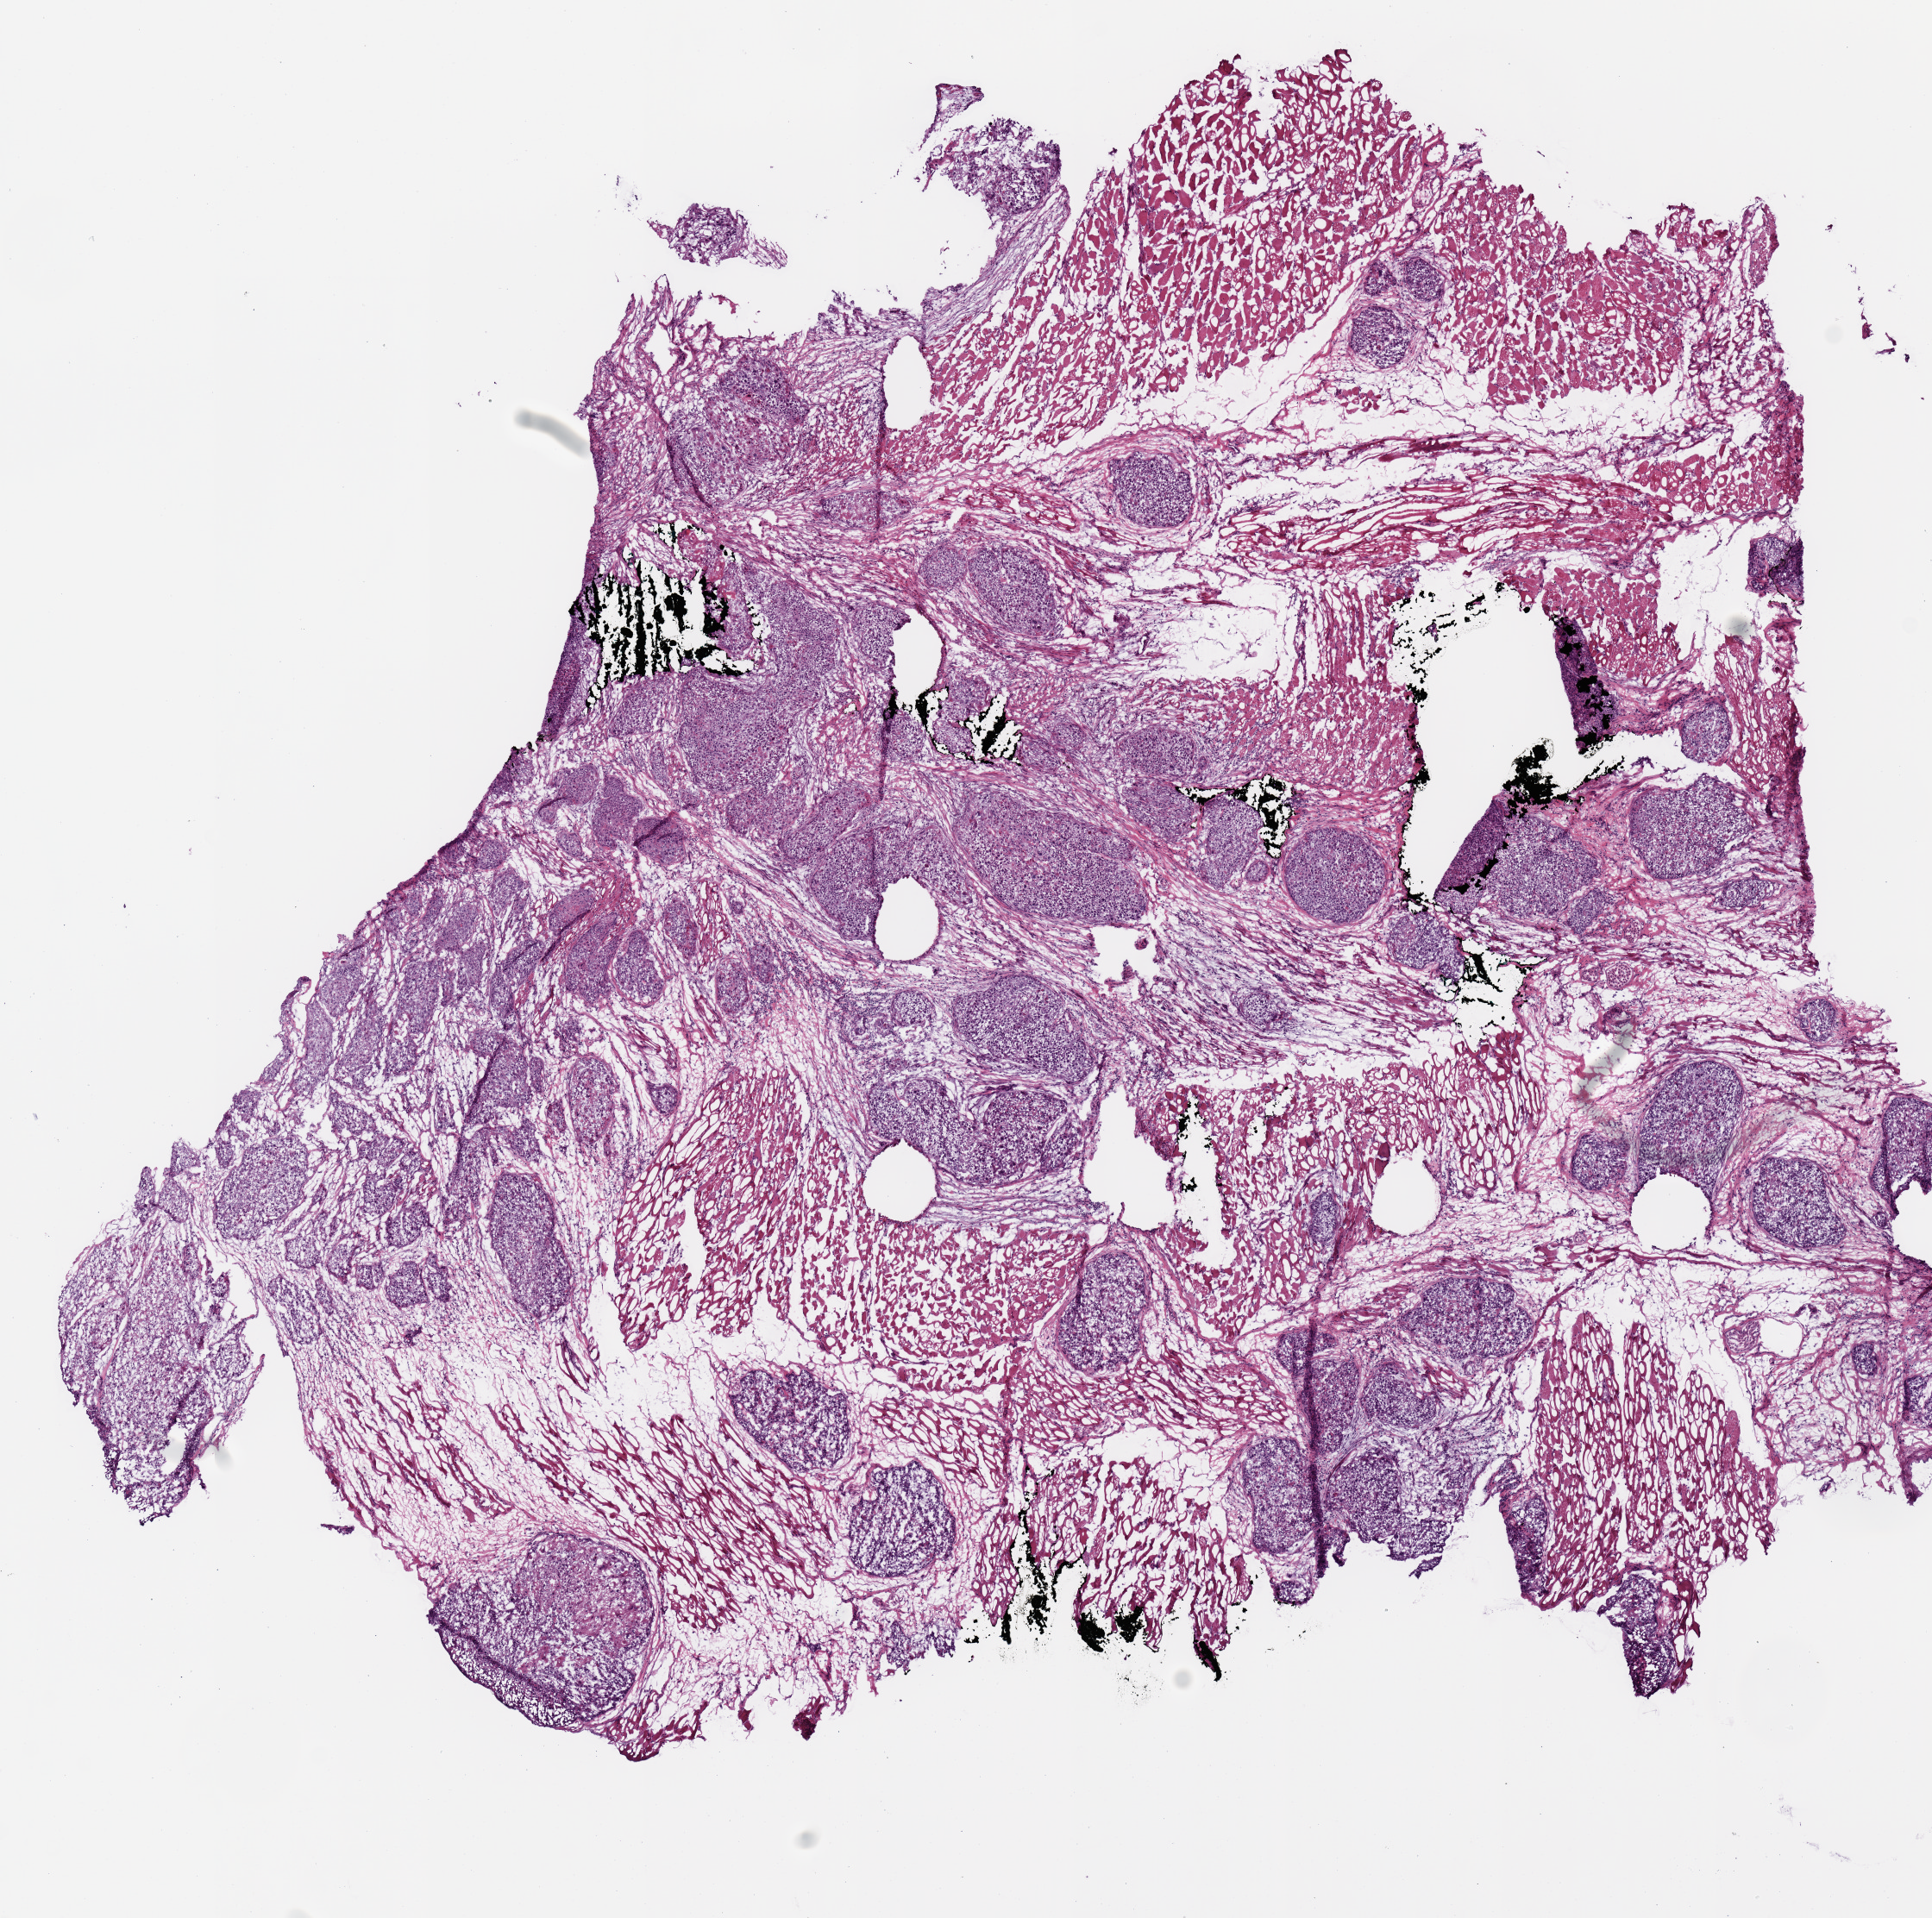
Digitized H&E-stained tissue section (whole slide), low-resolution overview of the scanned area, about 8.9 x 8.8 mm (slide scanned at 20x). Frozen section from the top of the tissue portion. Sample: primary tumour, head and neck. Male patient; age at initial diagnosis 63 years. Histologic grade: G3 (poorly differentiated). Composition of this section per pathologist review: tumour nuclei 70%, necrosis 0%.
Lymph nodes positive (case pathology): 0 of 57 examined. AJCC pathologic stage: IVA (7th edition). Histologic diagnosis: Squamous cell carcinoma, NOS. TNM: T3 N2c M0.